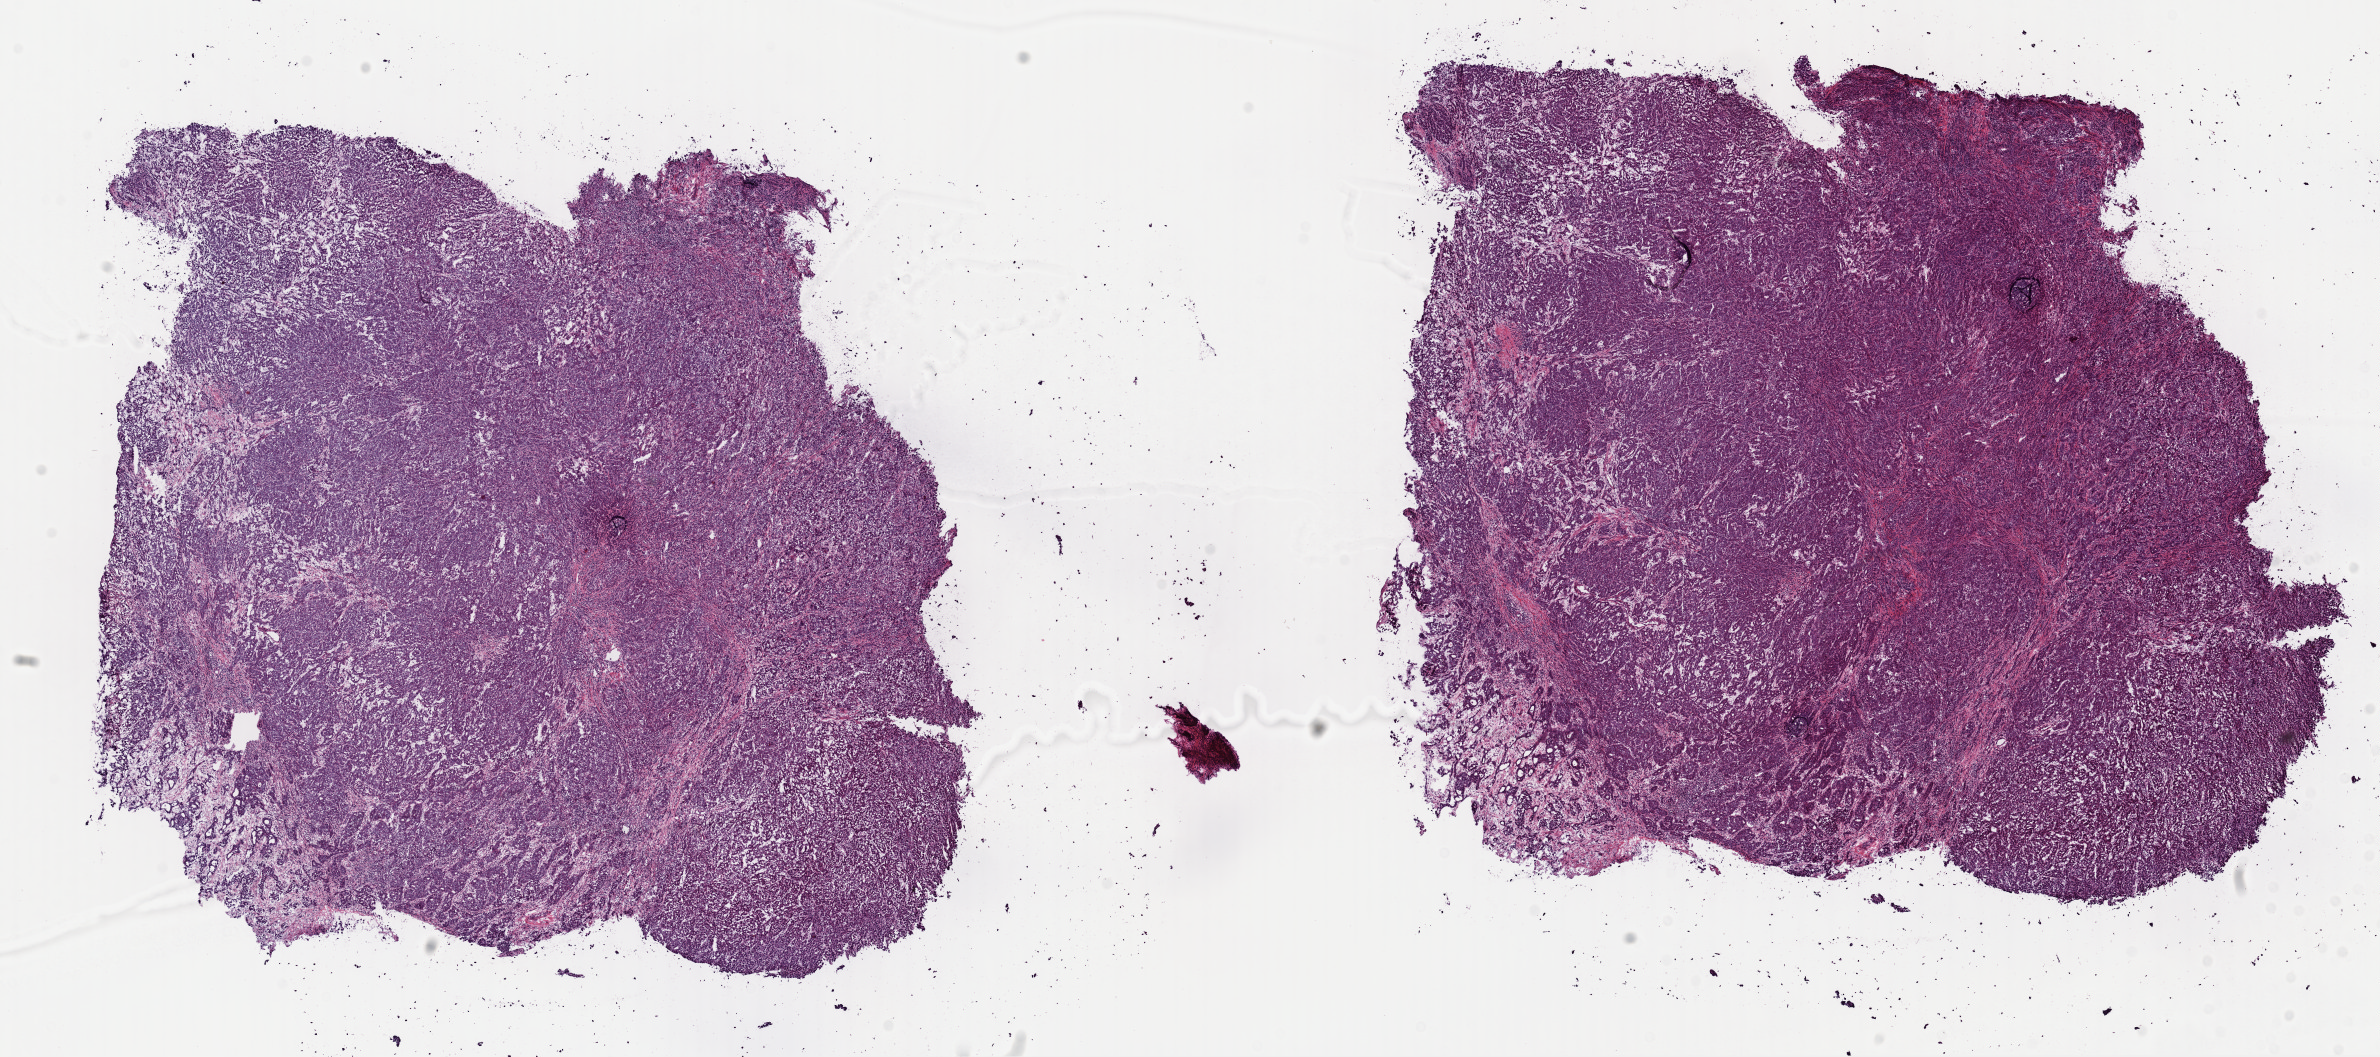
Digitized H&E tissue section (whole slide), whole scanned area (about 18.8 x 8.3 mm, from a 40x scan) shown as a low-resolution overview; frozen section from the top of the tissue portion; sample: primary tumour, liver. Female patient; age at initial diagnosis 74 years. Histologic grade: G3 (poorly differentiated). Composition of this section per pathologist review: tumour cells 95%, tumour nuclei 85%, normal cells 0%, stromal cells 4%, necrosis 1%. Inflammatory infiltration, as recorded: lymphocyte infiltration 10%, monocyte infiltration 1%, neutrophil infiltration 1%.
• AJCC pathologic stage: IIIA (6th edition)
• pathologic diagnosis: Hepatocellular carcinoma, NOS